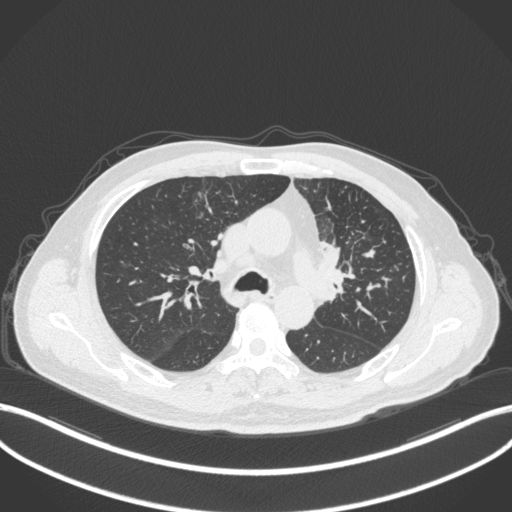
Chest CT, one axial slice; position 228 of 386 along the scan axis; reconstruction kernel B31f; lung window (W 1500 / L -600 HU); 512 × 512 image matrix. Male patient, age 69 years. From the clinical record (not read from this slice): clinical TNM (as recorded): T2a N2 M0.
Annotated regions visible in this slice (bounding box drawn by a radiologist):
- lung tumour (recorded histology: adenocarcinoma): bounding box <319,239,350,292> (left, top, right, bottom; pixels)